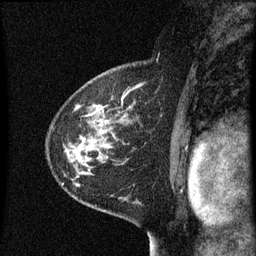
Breast MRI (dynamic contrast-enhanced), one sagittal slice; slice 41 of 60 in the series (ordered by position); dynamic contrast-enhanced series, image 2 of 3 at this slice position (ordered by acquisition); 1.5 T; TE 4.2 ms, TR 8 ms; 2 mm slice thickness; 256 × 256 image matrix, field of view 180 × 180 mm. Patient: female, 60 years.
Outlined on this slice (semi-automatically segmented with operator editing):
- analysis volume of interest (the breast-tissue region the enhancement analysis was run in; not a lesion): bounding box (x1, y1, x2, y2) in pixels: (49, 82, 137, 183)
- tumour enhancement mask (voxels above the 70 % enhancement threshold inside the analysis volume of interest): (91, 108, 103, 115)